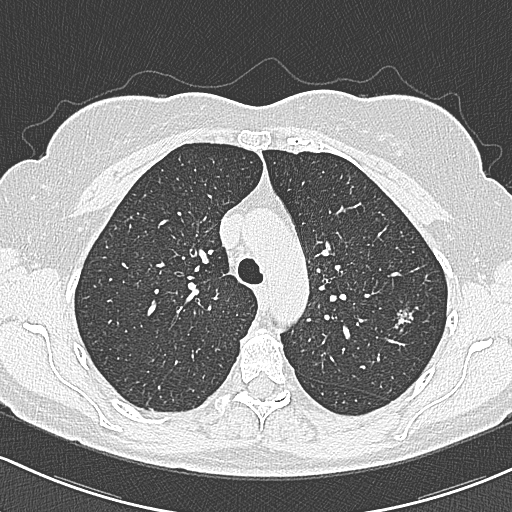
Axial slice from a low-dose chest CT screening exam; first (baseline) screen; lung window (W 1500 / L -600 HU); 120 kVp; 512 × 512 image matrix, field of view 318 × 318 mm. Female, age 65 years at enrolment. Current smoker at enrolment.
• Lesion marked by an expert reader, bounding box [x1, y1, x2, y2] px = [380, 298, 422, 338].
• The screening reader recorded 3 non-calcified nodules or masses ≥4 mm on this exam; which of them this box marks is not recorded.
• Later outcome: lung cancer diagnosed 390 days after this screen (after the second annual screen) — bronchiolo-alveolar carcinoma, non-mucinous, left upper lobe, stage IA (AJCC 6th edition), 10 mm at pathology.